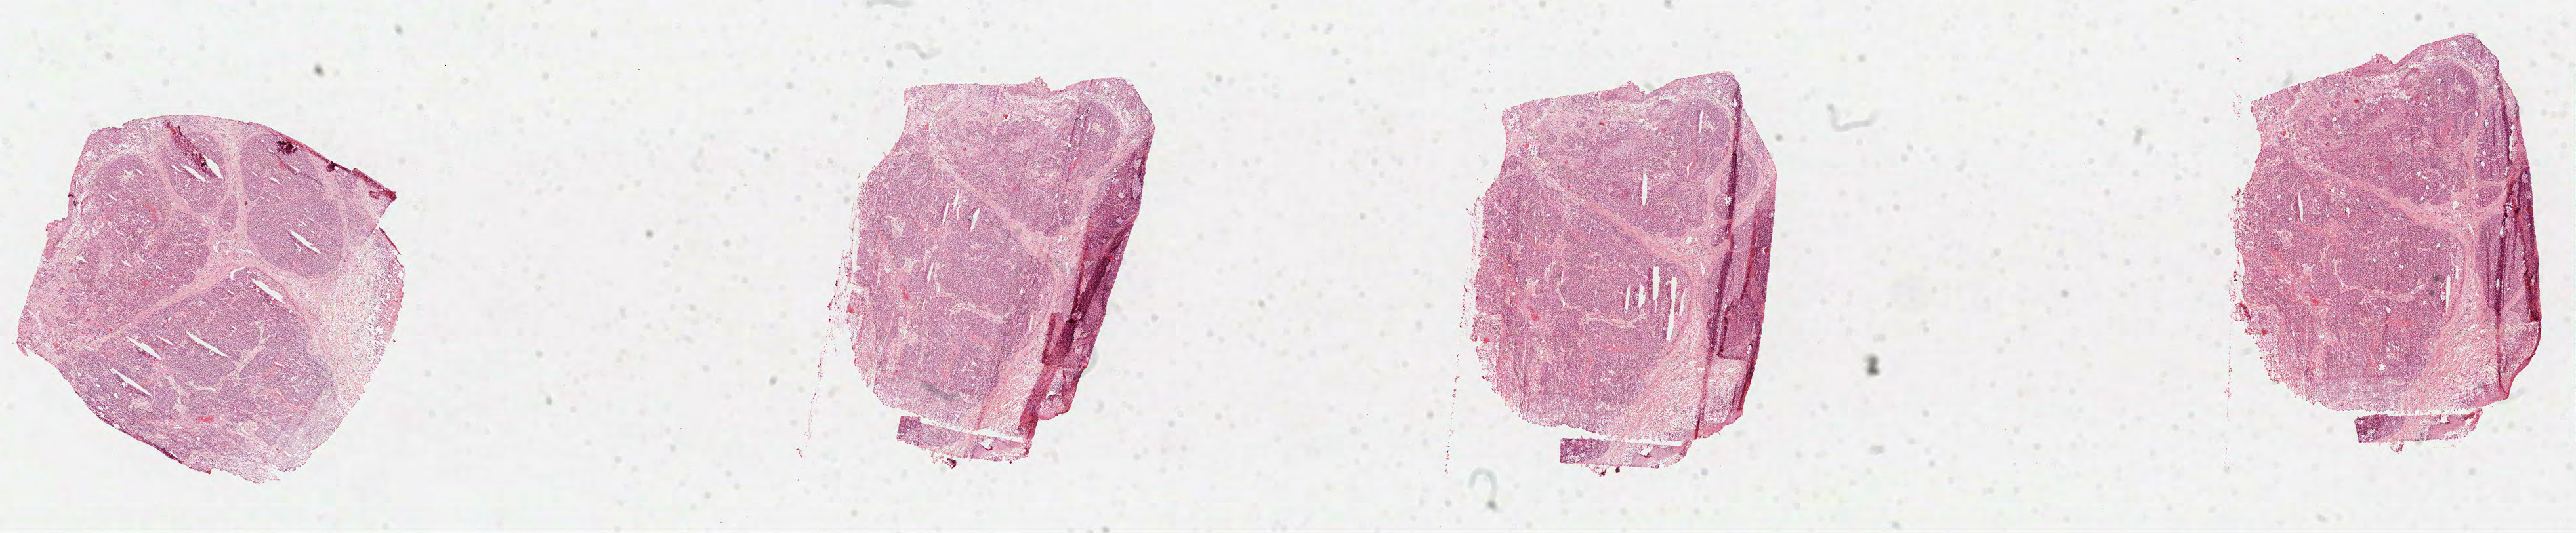
Digitized H&E tissue section (whole slide), whole scanned area (about 31.7 x 6.6 mm) shown as a low-resolution overview, FFPE section, head and neck, primary tumour sample. Female patient; age at initial diagnosis 55 years. Histologic grade: G3 (poorly differentiated).
Diagnosis: Squamous cell carcinoma, NOS (lip, NOS). AJCC pathologic stage: I.